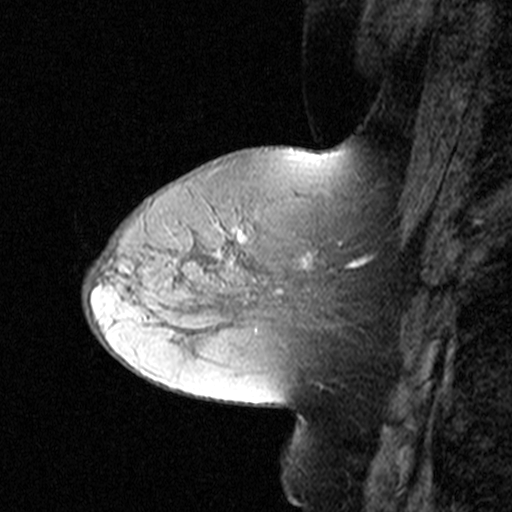
Breast MRI (dynamic contrast-enhanced), one sagittal slice. Position 16 of 44 along the scan axis. Dynamic contrast-enhanced study with each time point stored as its own series, time point 2 of 3 at this slice position (early post-contrast, ordered by acquisition time). 1.5 T. TE 4.5 ms, TR 11 ms. 512 × 512 image matrix, field of view 200 × 200 mm. Female patient, age 50 years. Case-level facts recorded for this patient, not image findings: setting: breast cancer imaged before/during neoadjuvant chemotherapy; receptor status: HR-positive, HER2-negative.
Outlined on this slice (semi-automatically segmented with operator editing):
- analysis volume of interest (the breast-tissue region the enhancement analysis was run in; not a lesion): bounding box [x1, y1, x2, y2] px = [180, 198, 318, 311]
- tumour enhancement mask (voxels above the 90 % enhancement threshold inside the analysis volume of interest): [219, 233, 313, 268]